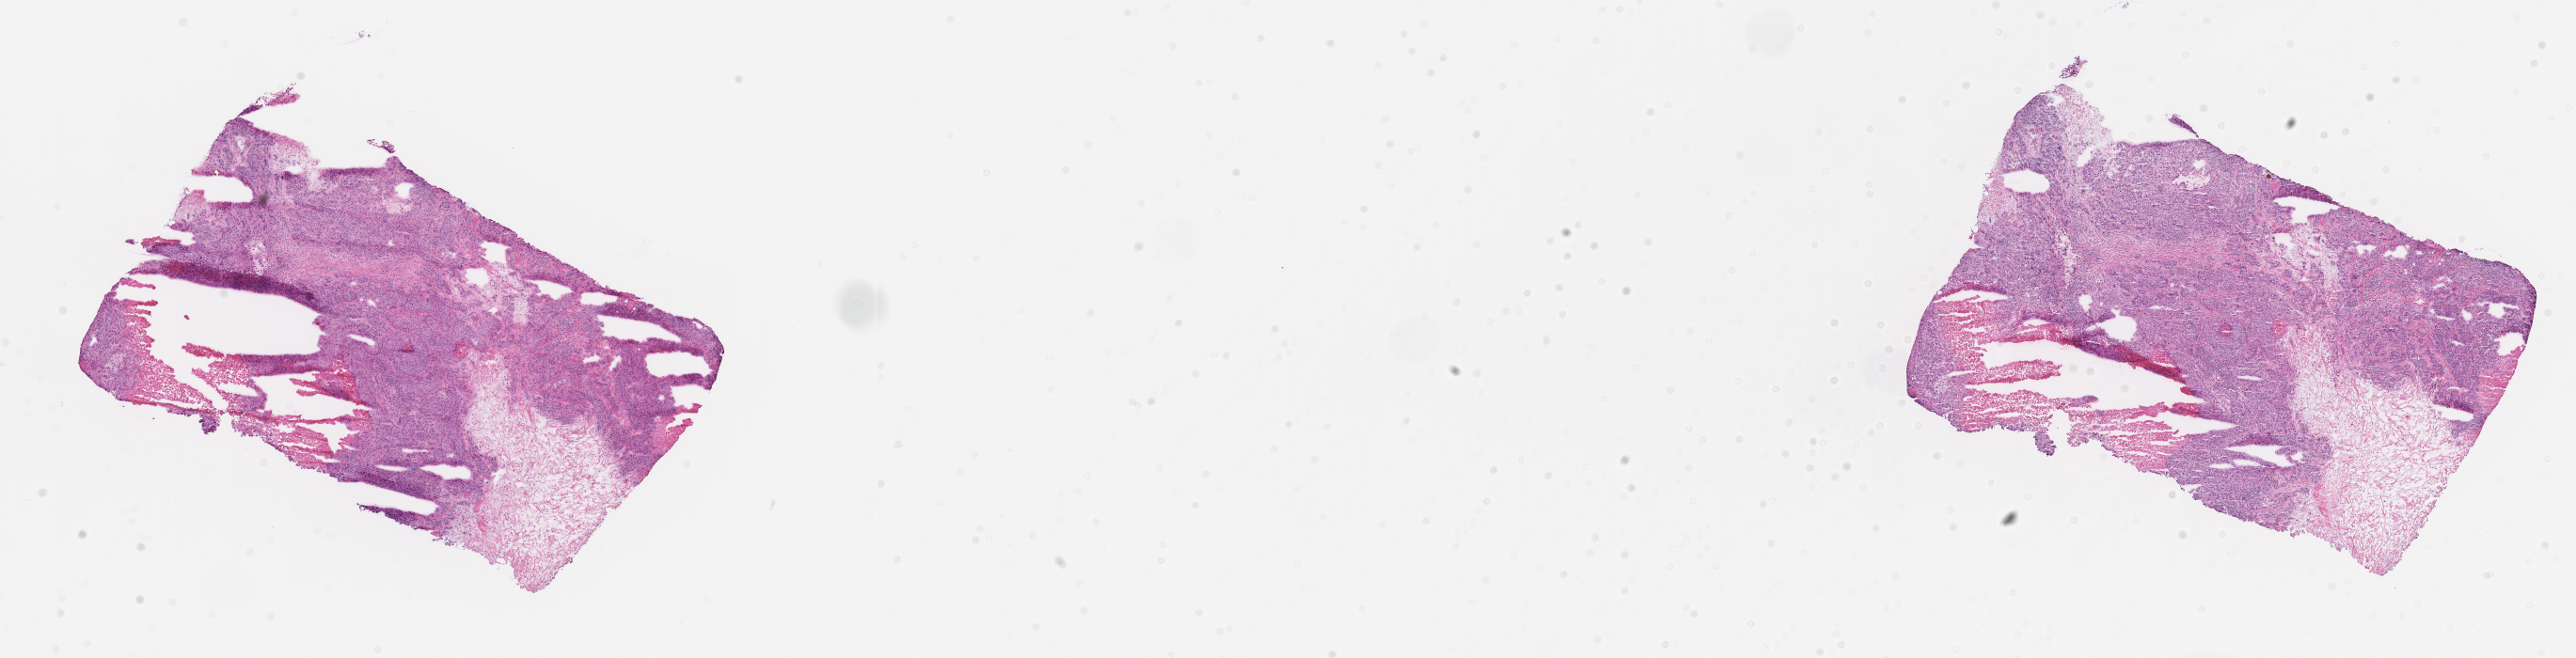
Digitized H&E-stained section, whole scanned area (about 22.1 x 5.6 mm) shown as a low-resolution overview. Cryosection. Primary tumor. Anatomic site: breast (right). Patient: female, age at initial diagnosis 74 years. Composition of this section per pathologist review: tumor cells 55%, tumor nuclei 70%, stromal cells 15%, necrosis 15%, normal cells 15%. Inflammatory infiltration, as recorded: lymphocyte infiltration 5%, monocyte infiltration 2%, neutrophil infiltration 0%.
* diagnosis: Infiltrating duct carcinoma, NOS